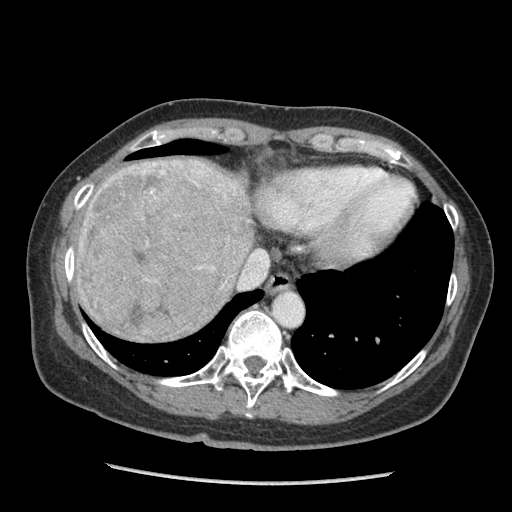
Contrast-enhanced abdominal CT (liver protocol), one axial slice. Position 79 of 105 along the scan axis. Reconstruction kernel STANDARD. 140 kVp. Soft-tissue window (W 400 / L 40 HU). 2.5 mm slice thickness. 512 × 512 image matrix, field of view 340 × 340 mm. From the clinical record (not read from this slice): diagnosis: hepatocellular carcinoma (patient treated with transarterial chemoembolisation; whether this scan precedes or follows treatment is not stated here); TNM stage (as recorded): Stage-I; Child-Pugh class: A; tumour differentiation: moderately differentiated.
Structures marked on this image (semi-automatically segmented with operator editing):
- liver parenchyma outside the tumour (the mass and vessels are separate outlines, so this box may not span the whole liver): box from (x=76, y=158) to (x=254, y=334) px
- mass: (x=77, y=160)–(x=232, y=342)
- liver vessels: (x=153, y=163)–(x=155, y=166)